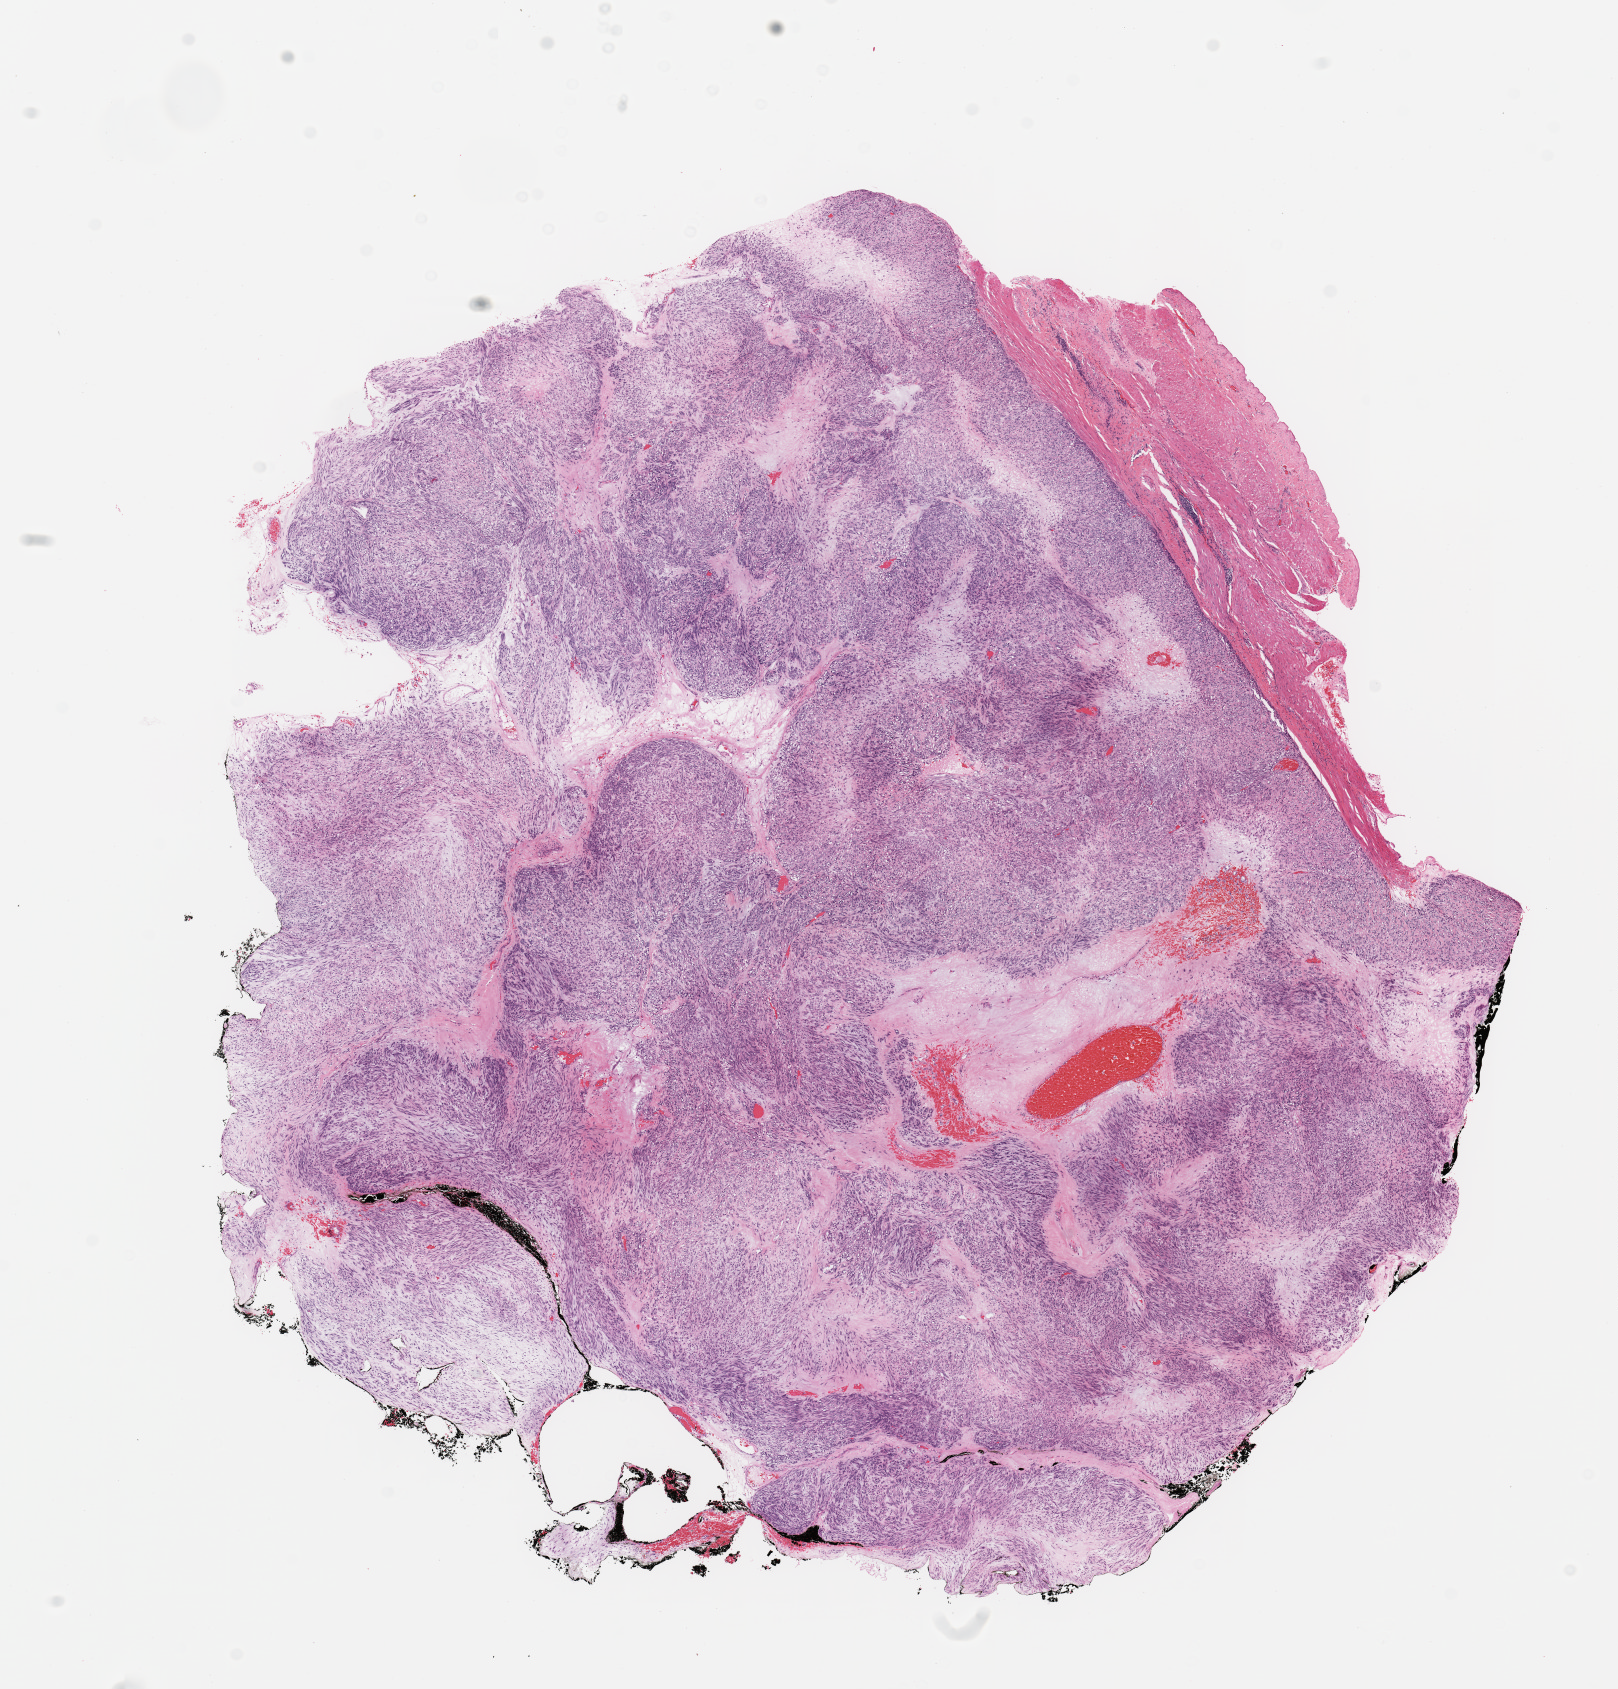
Hematoxylin and eosin (H&E) stained whole-slide image, low-resolution overview of the scanned area, about 12.8 x 13.4 mm. Female, 65 y/o.
Patient diagnosis (cohort enrolment): sarcoma (site not recorded at cohort level).